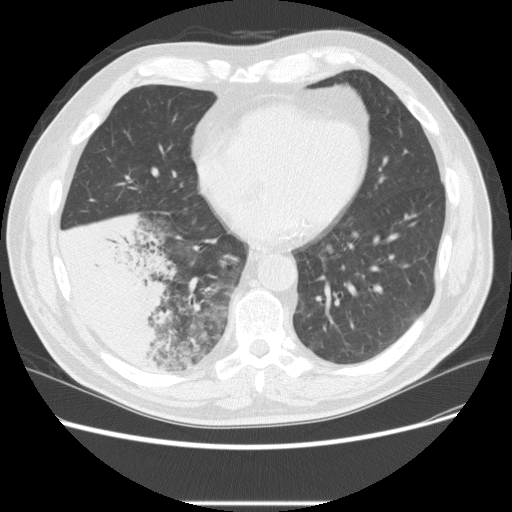
Low-dose screening chest CT, one axial slice. Slice 85 of 233 in the series (ordered by position). Reconstruction kernel STANDARD. 120 kVp. Lung window (W 1500 / L -600 HU). 2.5 mm slice thickness. 512 × 512 image matrix.
Annotated regions visible in this slice (outlined manually by an expert reader):
- lesion 3 (tumor, lower lobe of right lung): bounding box <57,210,177,366> (left, top, right, bottom; pixels)